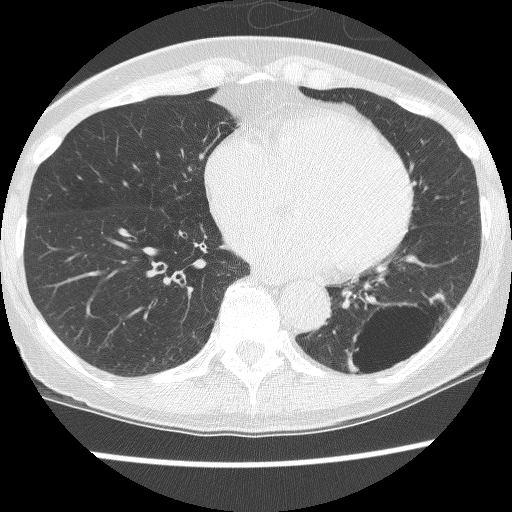
Axial slice from a low-dose chest CT screening exam. Third screening round (two years after baseline). Lung window (W 1500 / L -600 HU). Lung (sharp) reconstruction kernel (BONE). Slice 83 of 130 in the series. 512 × 512 image matrix. Female participant, aged 61 years at enrolment. Current smoker at enrolment.
Expert-annotated lung lesion, bounding box [x1, y1, x2, y2] px = [330, 290, 449, 390]. The screening reader recorded 2 non-calcified nodules or masses ≥4 mm on this exam (left lower lobe, left lower lobe); which of them this box marks is not recorded. Official screen result: positive, no significant change: stable abnormalities potentially related to lung cancer, unchanged since the prior screening exam. Lung cancer was diagnosed 166 days after this screen: non-small cell carcinoma, left lower lobe, poorly differentiated (G3), stage IB (AJCC 6th edition), 100 mm at pathology.